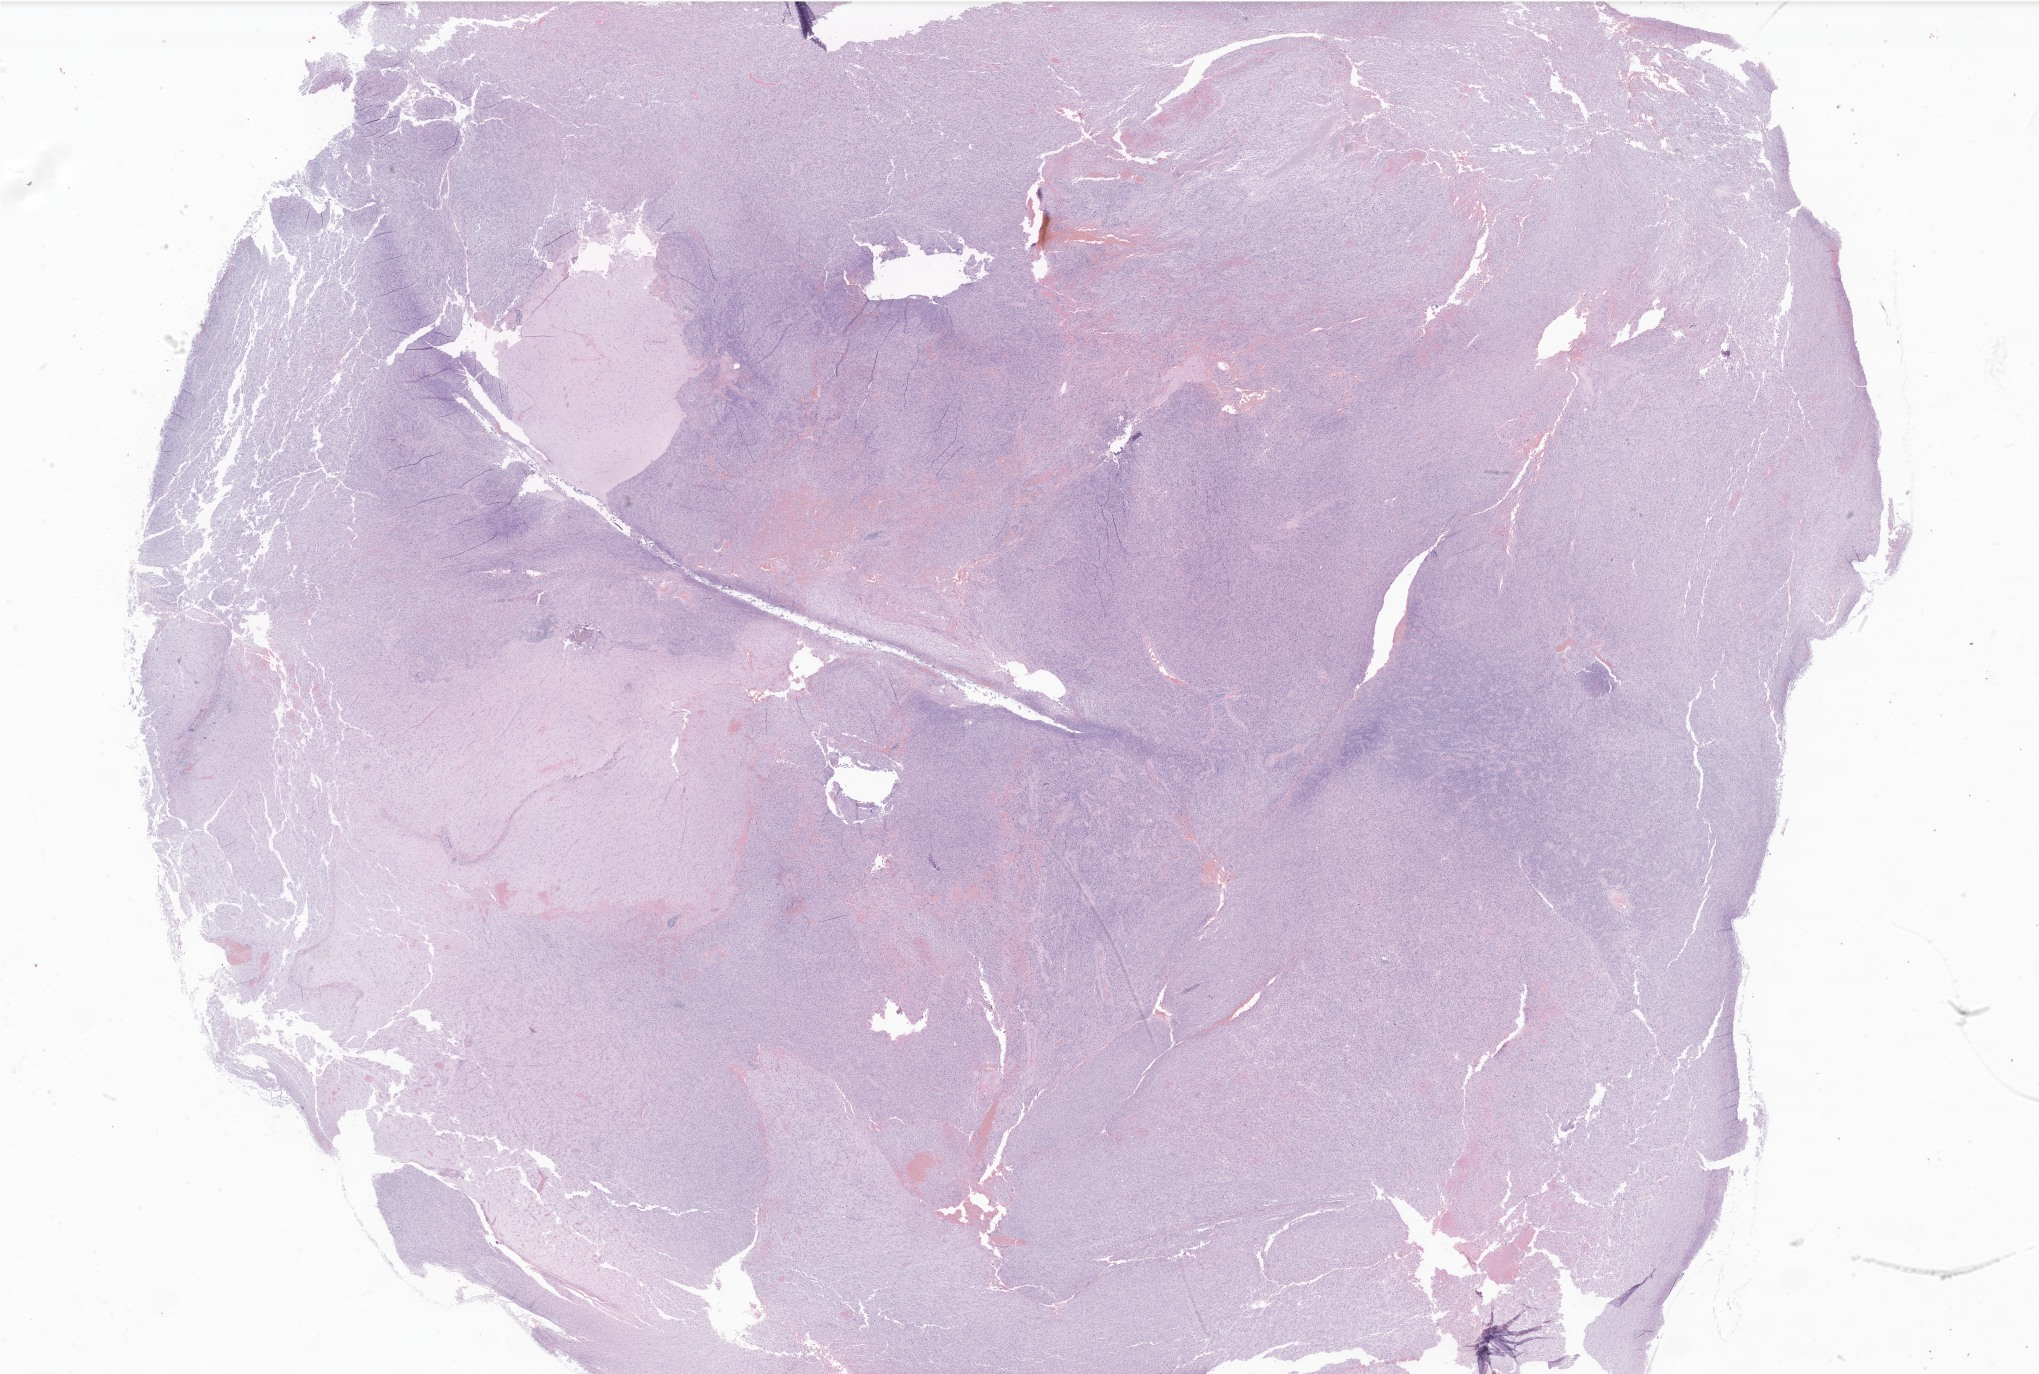
Digitized haematoxylin and eosin-stained section of tumor tissue from the brain, a low-resolution overview of the entire scanned area, about 34.4 x 23.2 mm, formalin-fixed paraffin-embedded section. Male patient, age 167 months (13 years 11 months).
* recorded diagnosis: Glioma, malignant